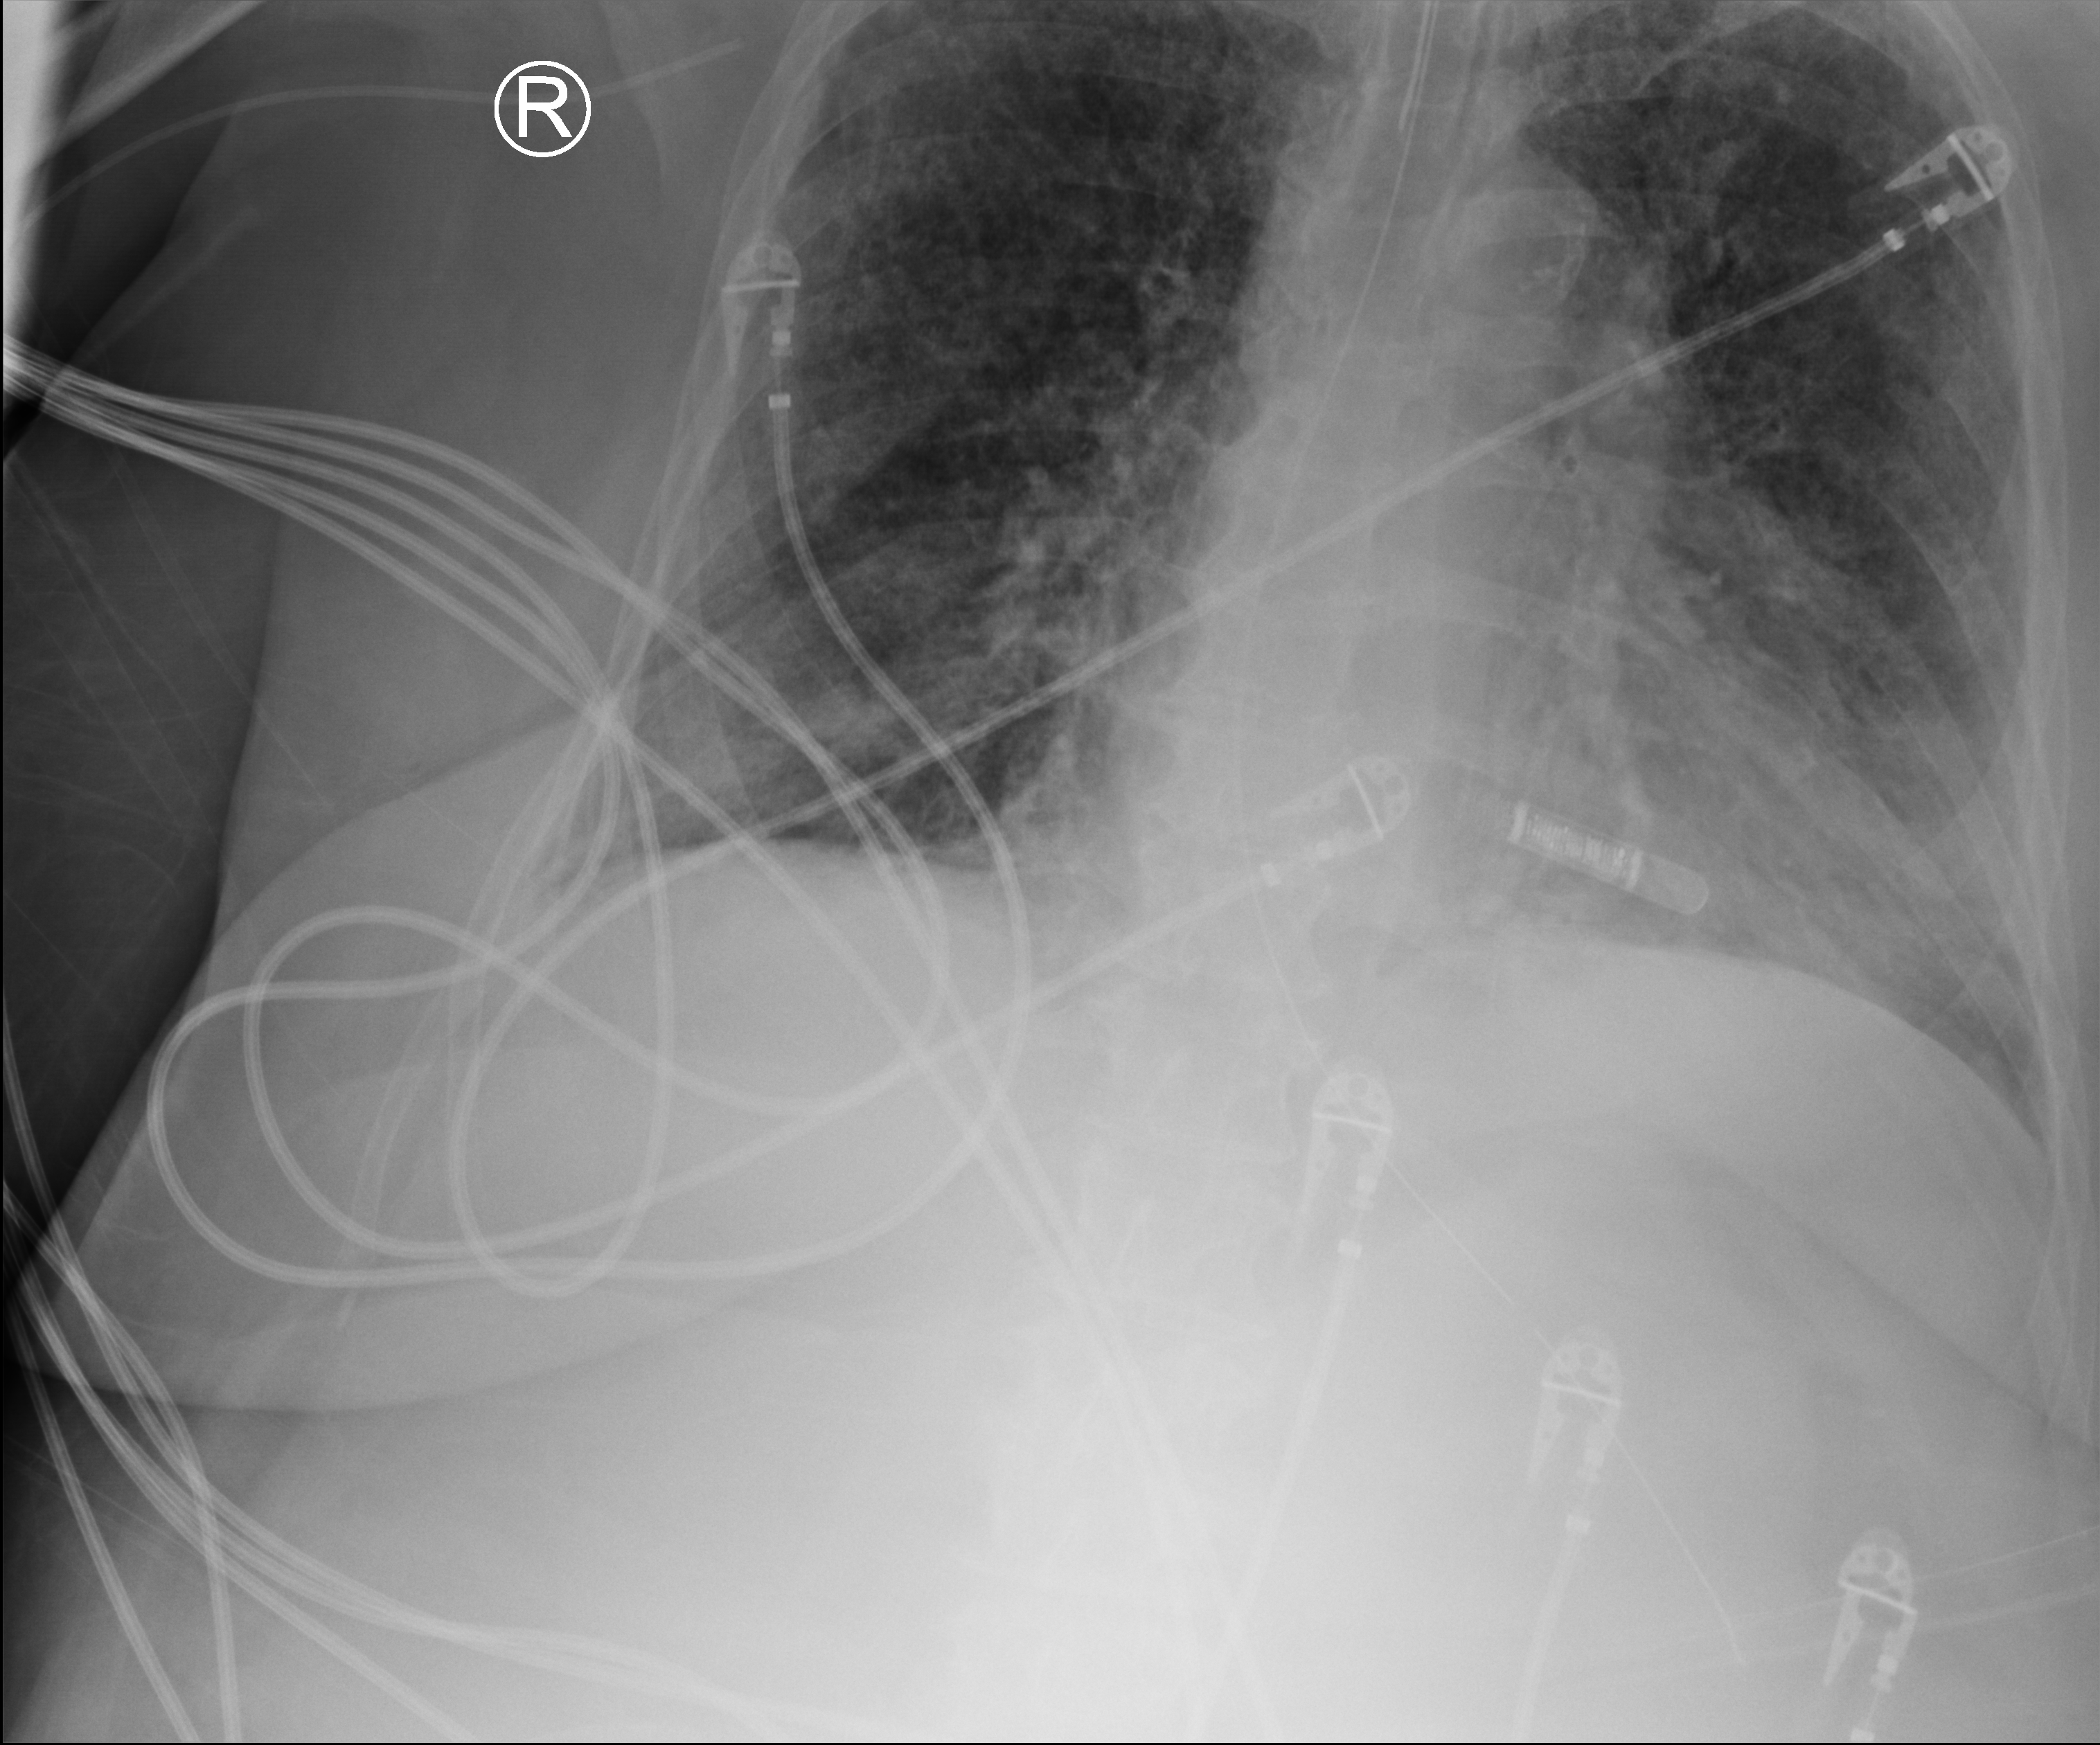
Chest X-ray (portable). Female patient hospitalised with COVID-19, age 60–74 years.
Hospital-stay facts (about this admission, not read from this image; timing relative to this image not recorded): admitted to intensive care during this hospital stay: yes; hypertension (admission record): yes.